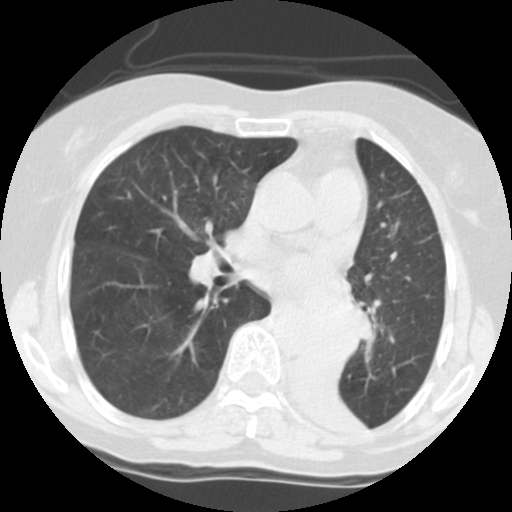
Chest CT (low-dose screening protocol), one axial image; third annual screen; lung window (W 1500 / L -600 HU); standard (soft-tissue) reconstruction kernel (STANDARD); 140 kVp; slice 67 of 113 in the series; 512 × 512 image matrix. Female participant, aged 56 years at enrolment. Former smoker at enrolment.
Expert-annotated lung lesion, box from (x=305, y=301) to (x=369, y=357) px. Screening reader's record for this exam: no non-calcified nodule ≥4 mm recorded. Official screen result: positive, other. Participant outcome: lung cancer diagnosed 9 days after this screen — squamous cell carcinoma, NOS, left main stem bronchus, poorly differentiated (G3), stage IIIA (AJCC 6th edition).